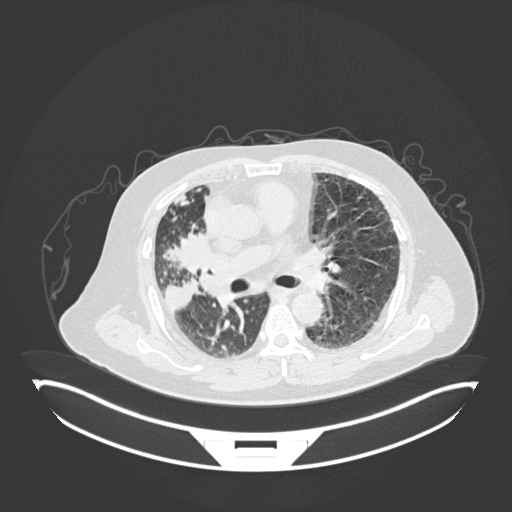
Chest CT, one axial slice; slice 93 of 201 in the series (ordered by position); lung window (W 1500 / L -600 HU); 1 mm slice thickness; 512 × 512 image matrix, field of view 500 × 500 mm. Male patient, age 69 years. From the clinical record (not read from this slice): clinical TNM (as recorded): T4 N3 M1.
Annotated regions visible in this slice (rectangle marked by the reading radiologist):
- lung tumour (recorded histology: adenocarcinoma): box from (x=167, y=228) to (x=219, y=285) px